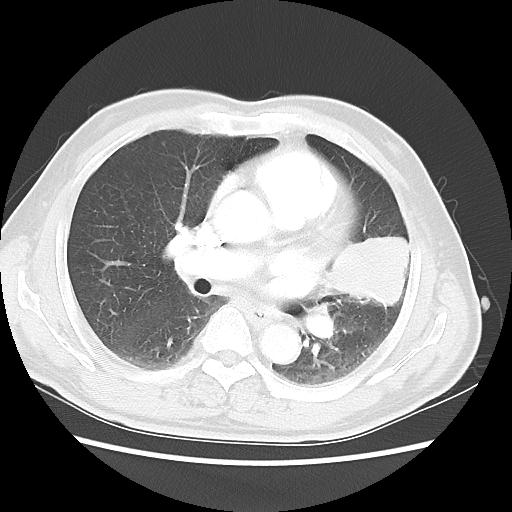
Chest CT, one axial slice. Lung window (W 1500 / L -600 HU). 5 mm slice thickness. 512 × 512 image matrix, field of view 360 × 360 mm. Male patient, age 69 years. Case-level facts recorded for this patient, not image findings: clinical TNM (as recorded): T3 N1 M1a.
Annotated regions visible in this slice (rectangle marked by the reading radiologist):
- lung tumour (recorded histology: squamous cell carcinoma): box from (x=331, y=227) to (x=416, y=310) px